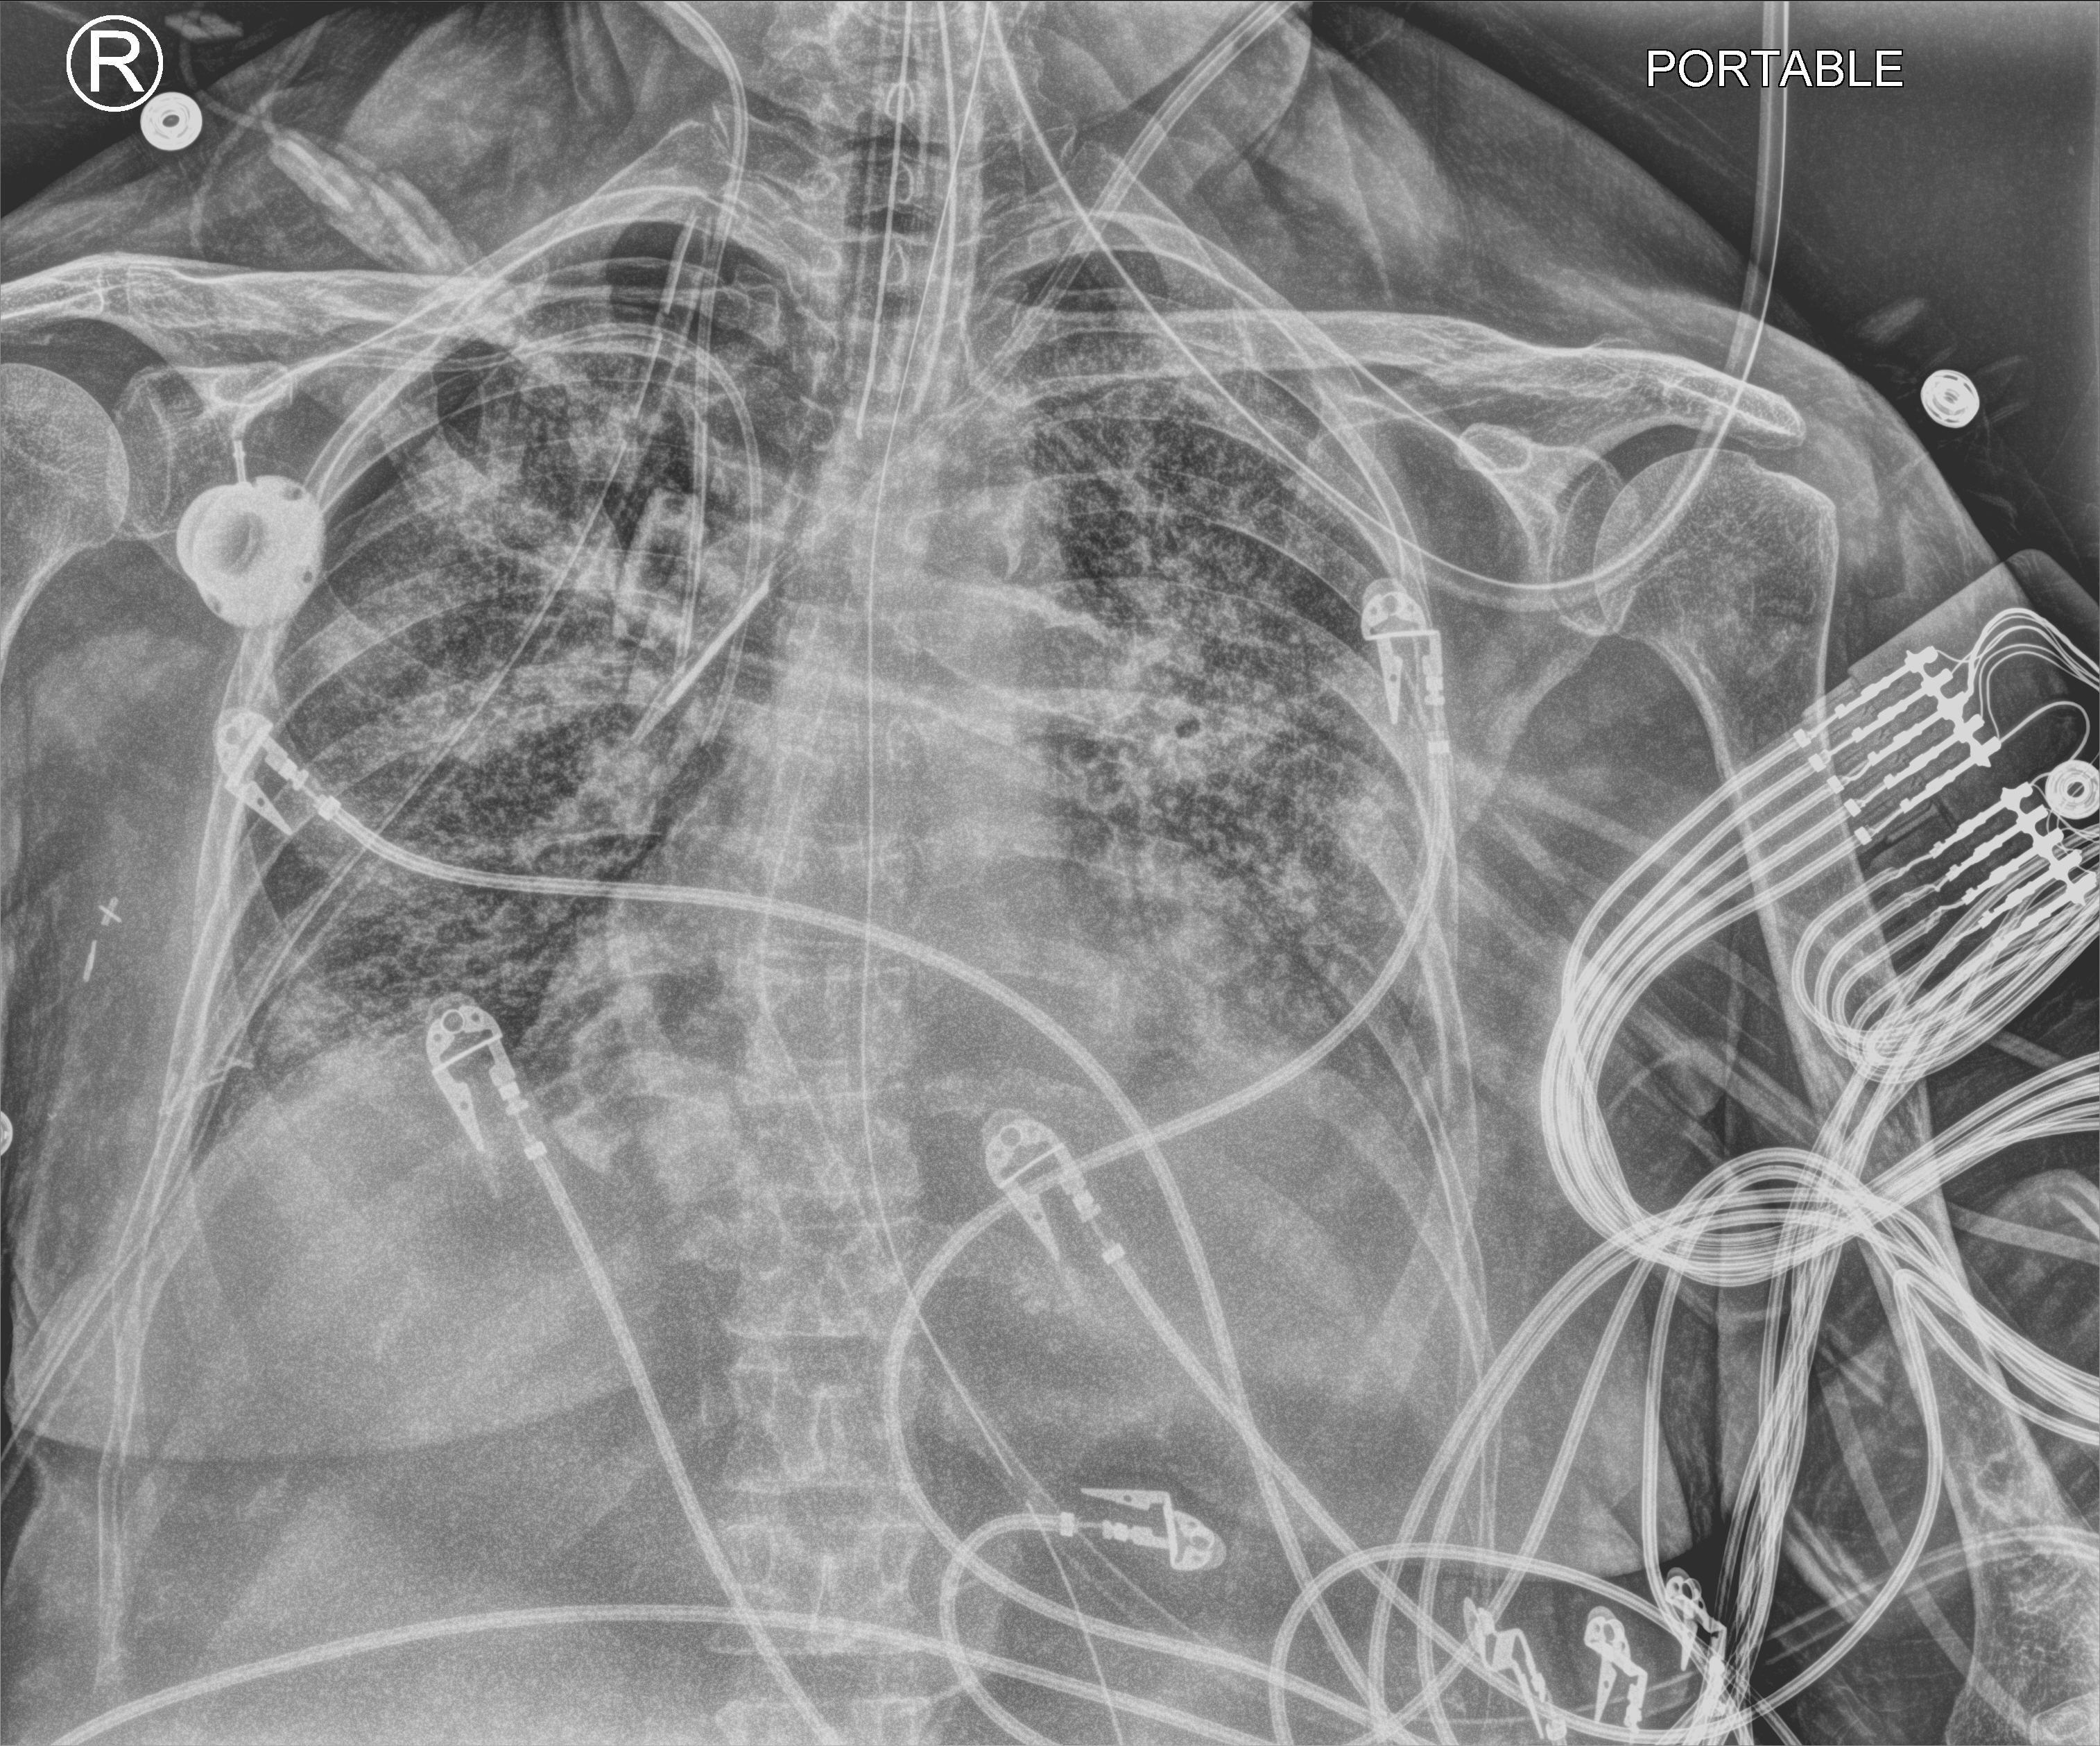
Chest X-ray (portable), anteroposterior (AP) projection. Female patient hospitalised with COVID-19, age 60–74 years.
Hospital-stay facts (about this admission, not read from this image; timing relative to this image not recorded):
- chronic kidney disease (admission record): no
- admitted to intensive care during this hospital stay: yes
- mechanically ventilated during this hospital stay: yes